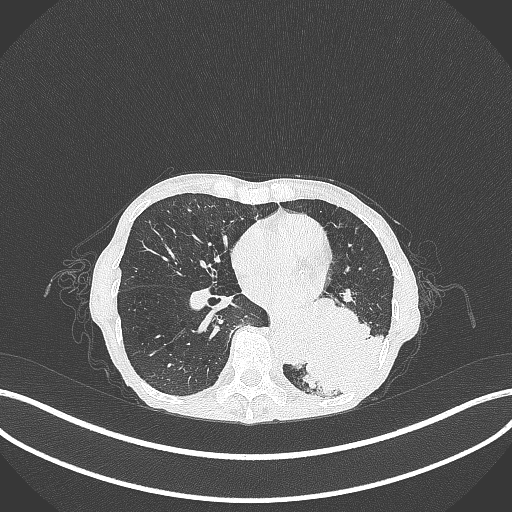
Chest CT, one axial slice; position 116 of 347 along the scan axis; 120 kVp; lung window (W 1500 / L -600 HU); 1 mm slice thickness; 512 × 512 image matrix. Female patient, age 70 years. Case-level facts recorded for this patient, not image findings: clinical TNM (as recorded): T3 N0 M0; histopathological grade: G3.
Annotated regions visible in this slice (rectangle marked by the reading radiologist):
- lung tumour (recorded histology: small cell carcinoma): box from (x=290, y=301) to (x=387, y=395) px